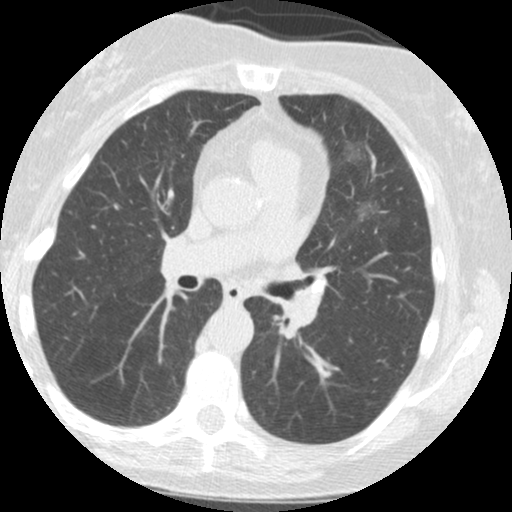
Low-dose screening chest CT, axial slice; first (baseline) screen; lung window (W 1500 / L -600 HU); standard (soft-tissue) reconstruction kernel (STANDARD). Female participant, aged 61 years at enrolment.
Lesion marked by an expert reader, bounding box [x1, y1, x2, y2] px = [303, 343, 352, 393]. Screening reader's record for this exam (one nodule recorded; not confirmed to be the boxed lesion): non-calcified nodule or mass ≥4 mm, left lower lobe, 12 × 11 mm, spiculated (stellate) margins, soft tissue attenuation. Later outcome: lung cancer diagnosed 440 days after this screen (after the second annual screen) — squamous cell carcinoma, NOS, left lower lobe, moderately differentiated (G2), stage IA (AJCC 6th edition), 12 mm at pathology.